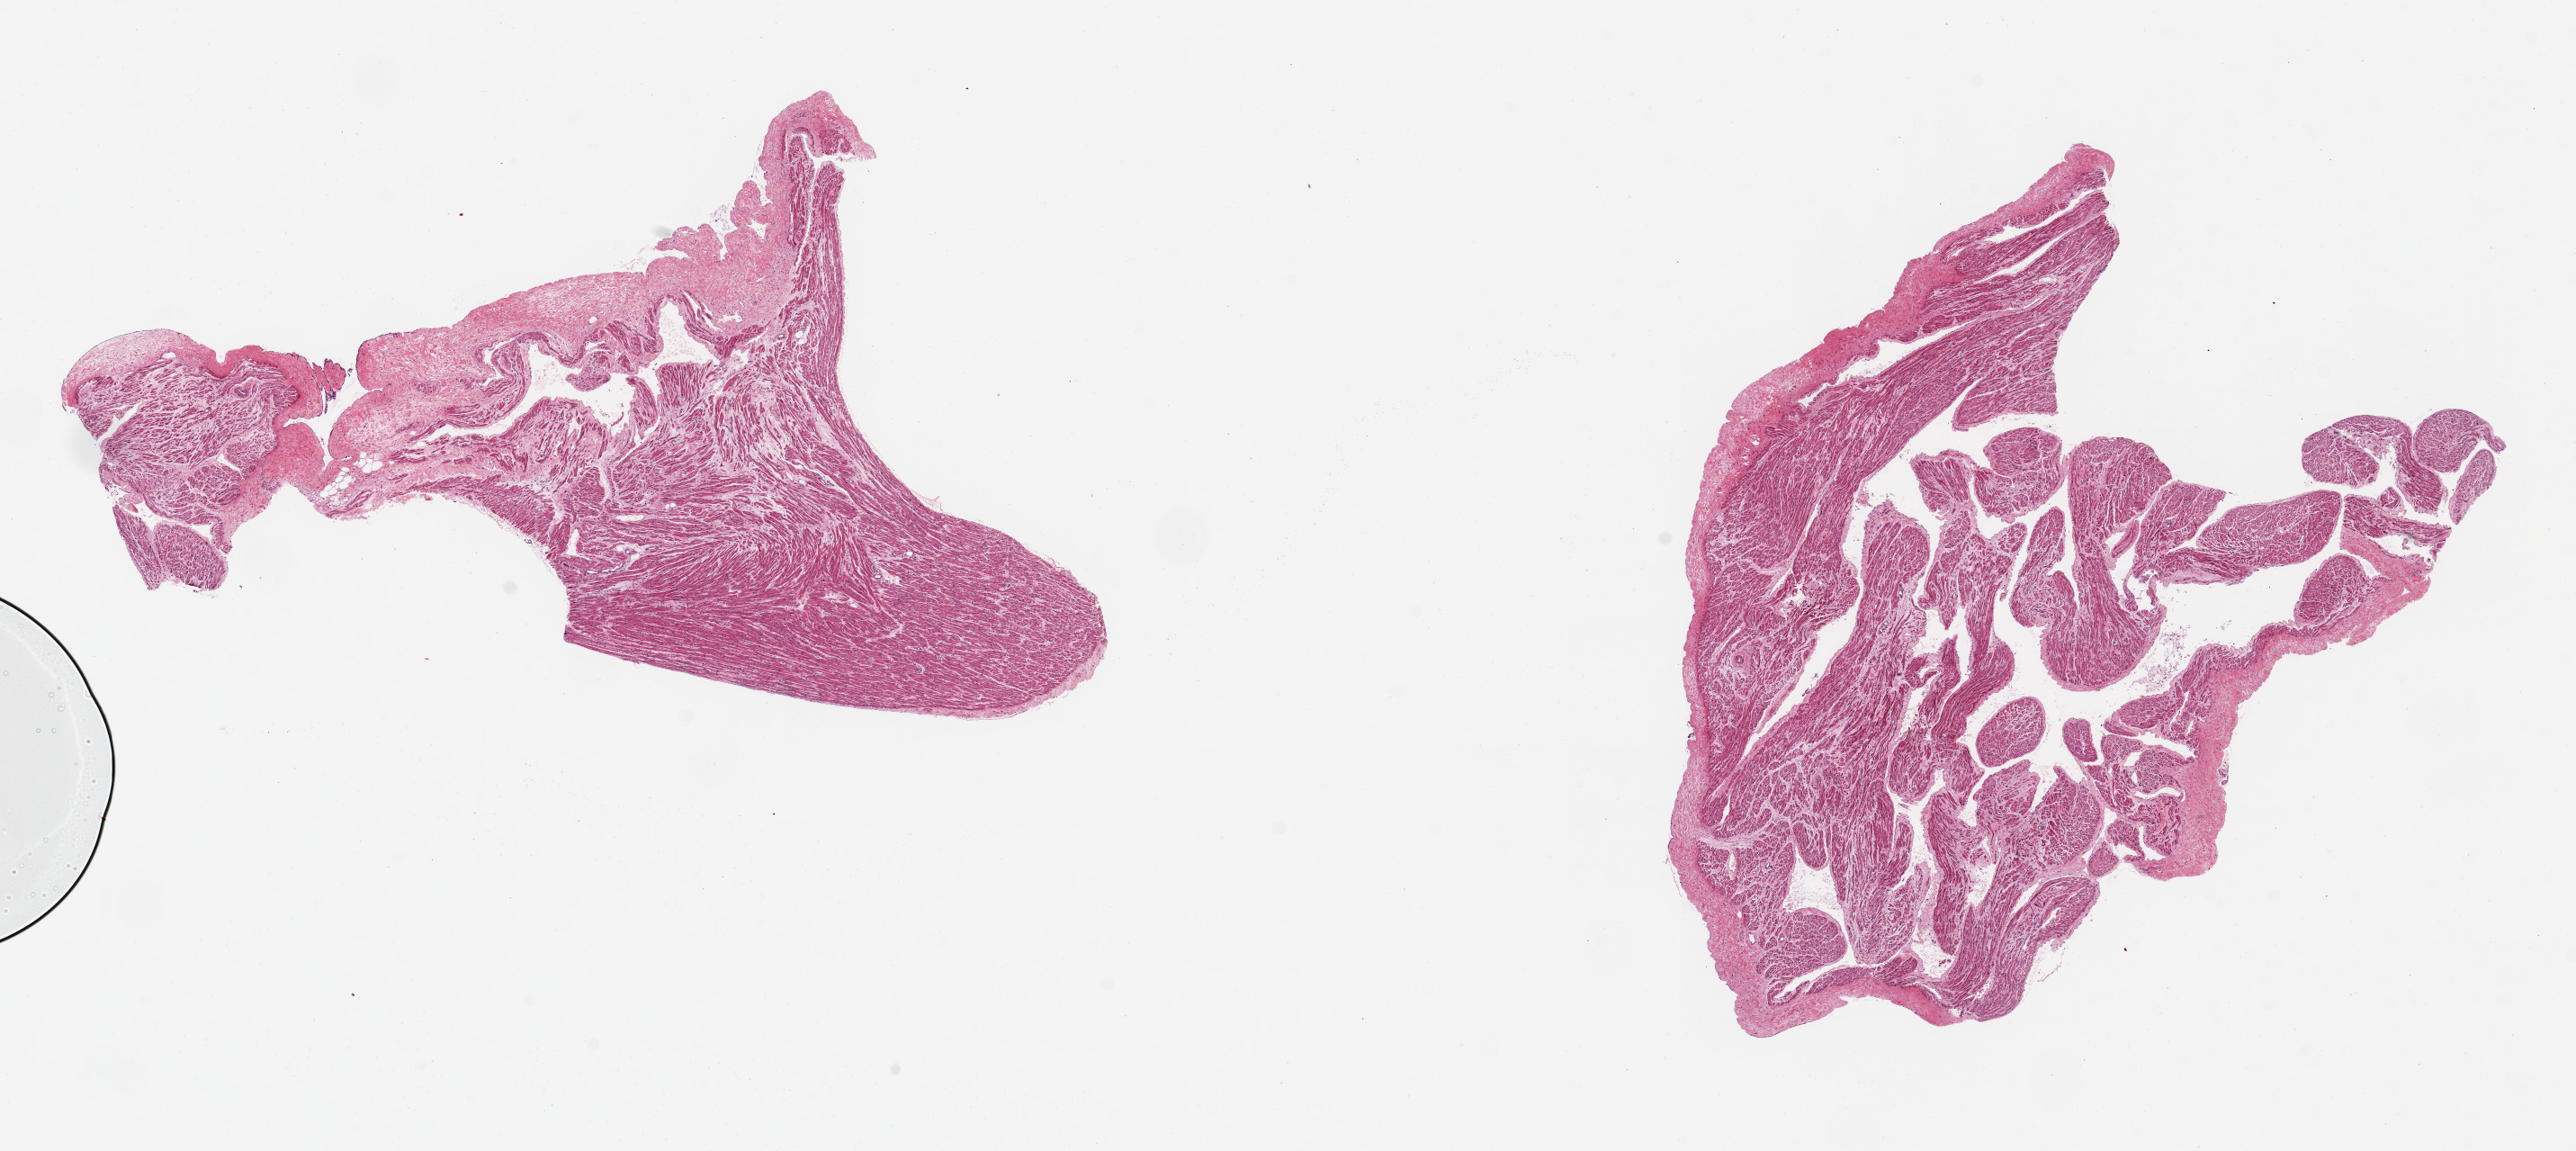
Whole-slide image, haematoxylin and eosin stain — low-resolution overview of the scanned area, about 22.6 x 10.1 mm, PAXgene-fixed paraffin-embedded (PFPE) section, sampled site (target tissue): auricular appendage, donor tissue sample. Donor sex: male.
Reviewer comment on this tissue sample: 2 pieces ~9x4mm.